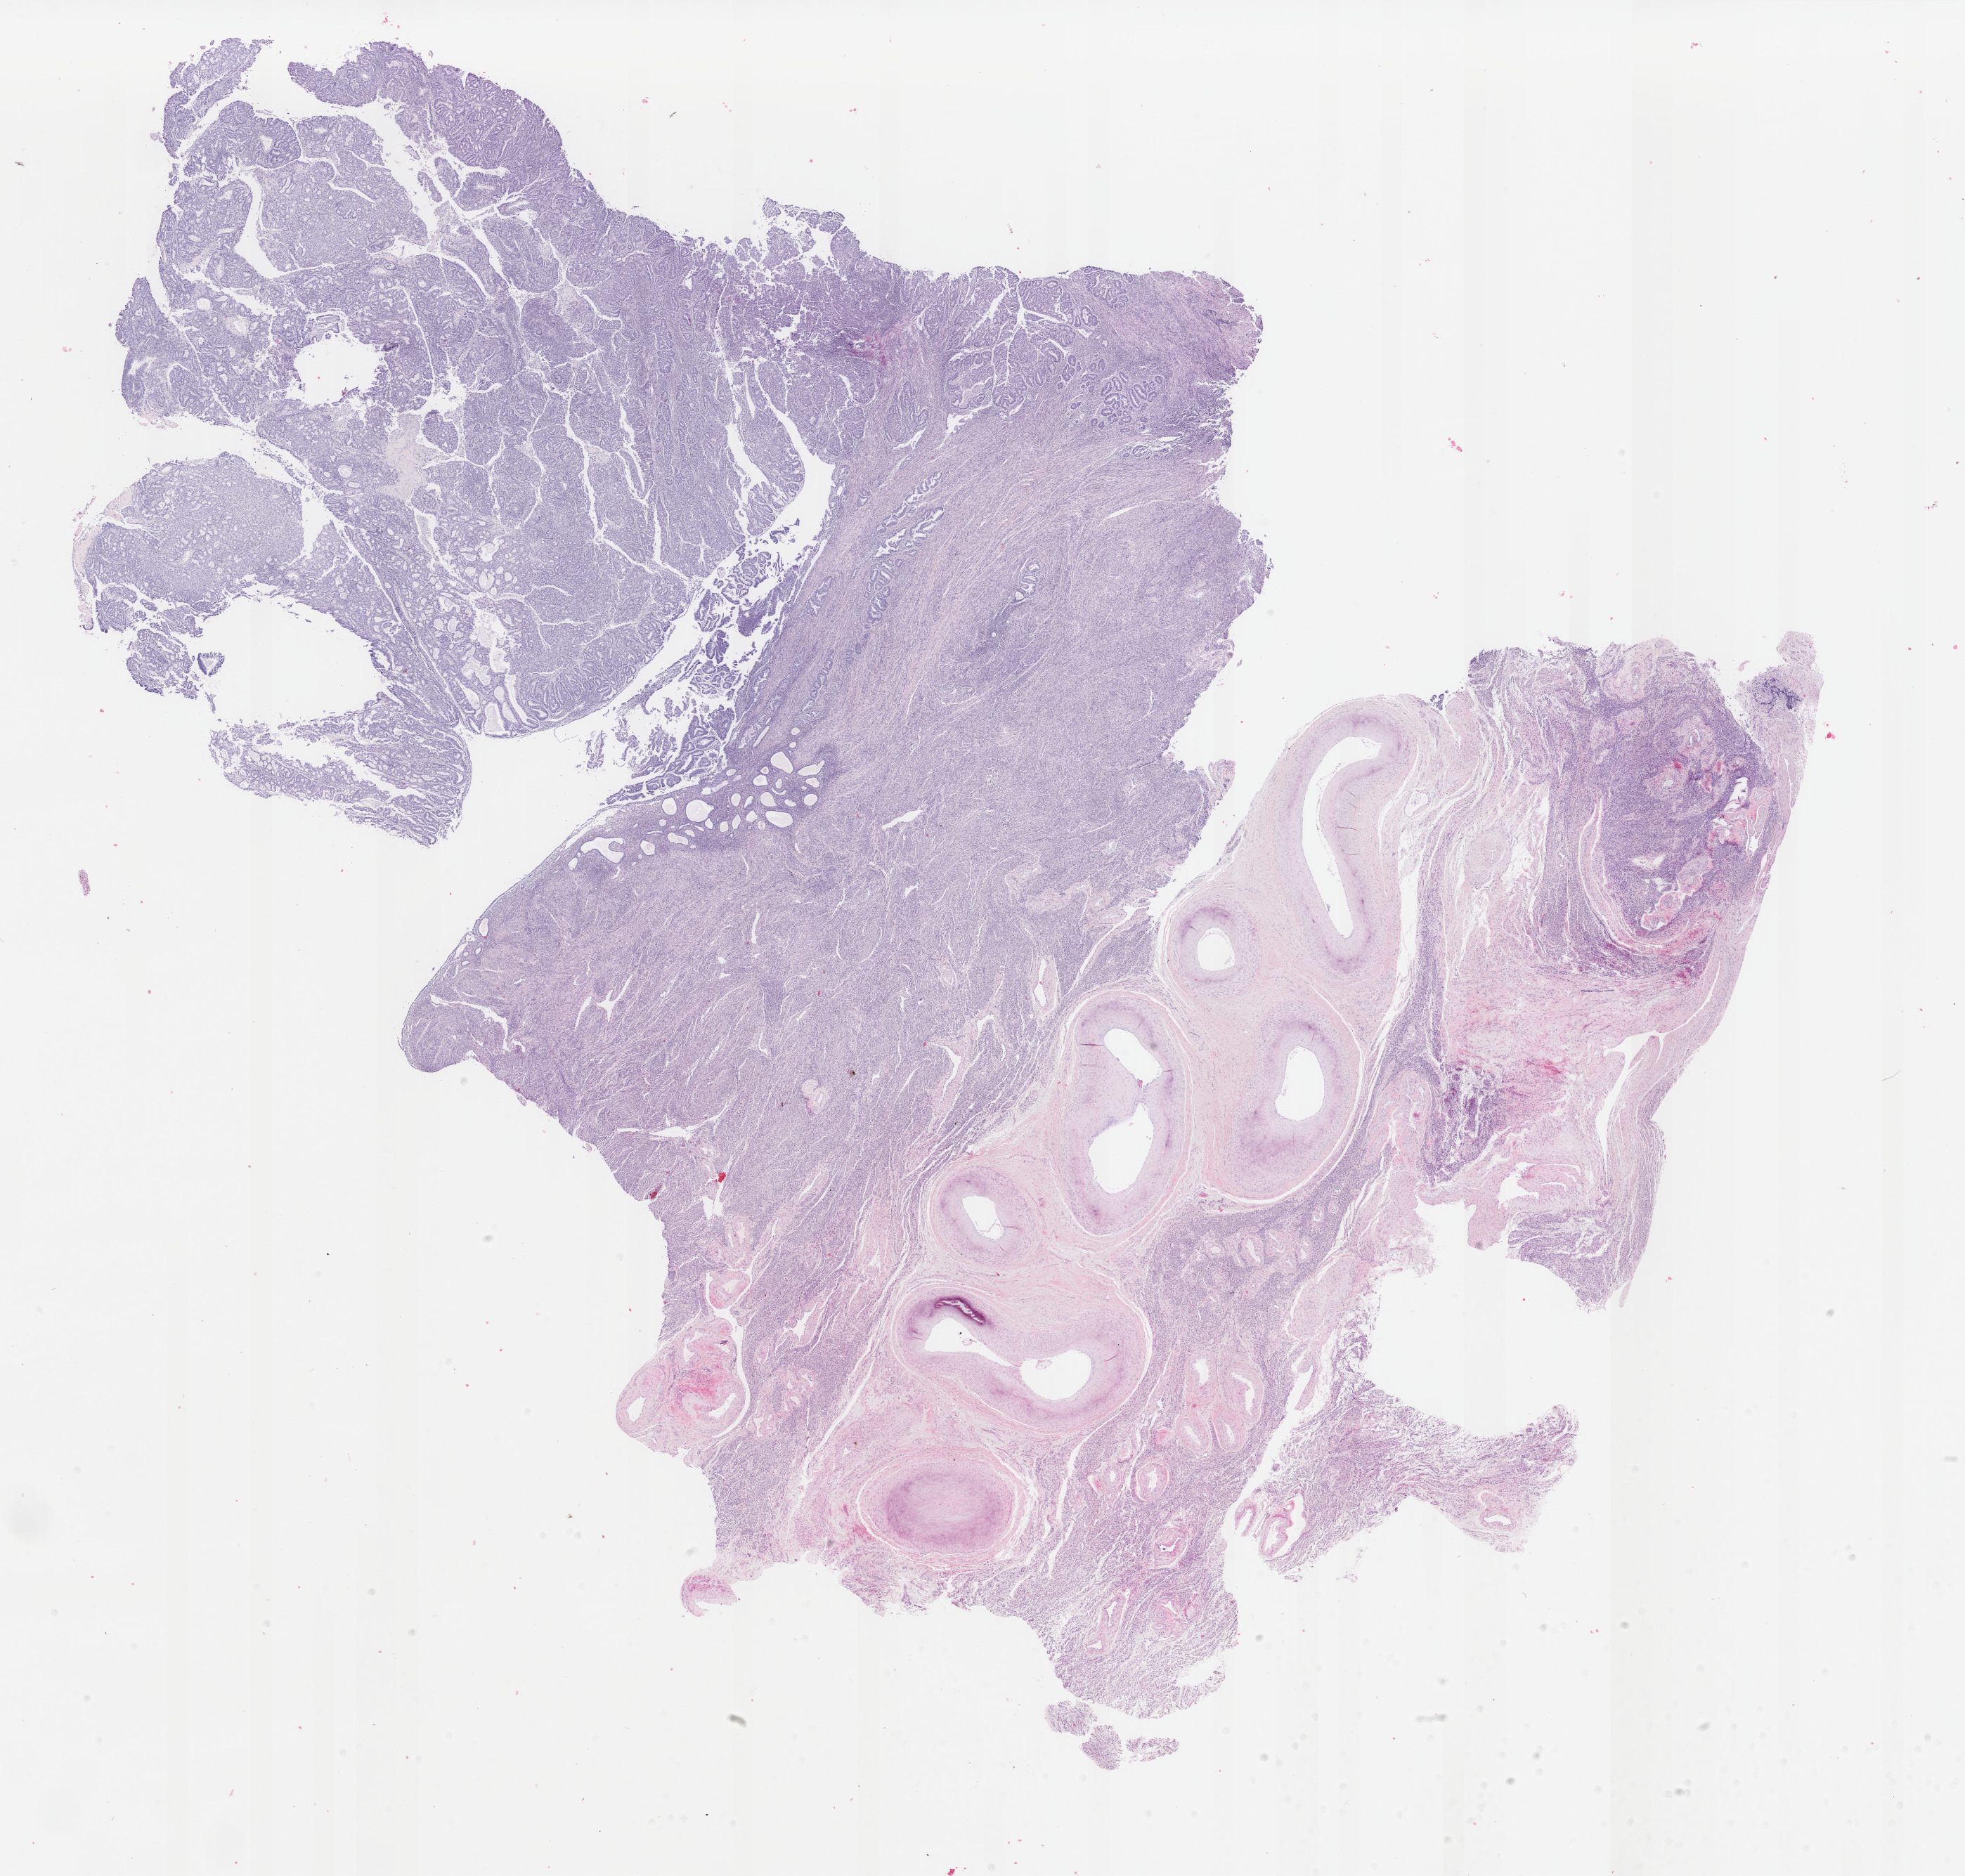
Digitized H&E-stained tissue section (whole slide), a low-resolution overview of the entire scanned area, about 22.2 x 21.2 mm; FFPE section; sample: primary tumour, uterus. Female, age 67 years at initial diagnosis. Histologic grade: G2 (moderately differentiated).
Histologic diagnosis: Endometrioid adenocarcinoma, NOS (endometrium). FIGO stage: IIIA.